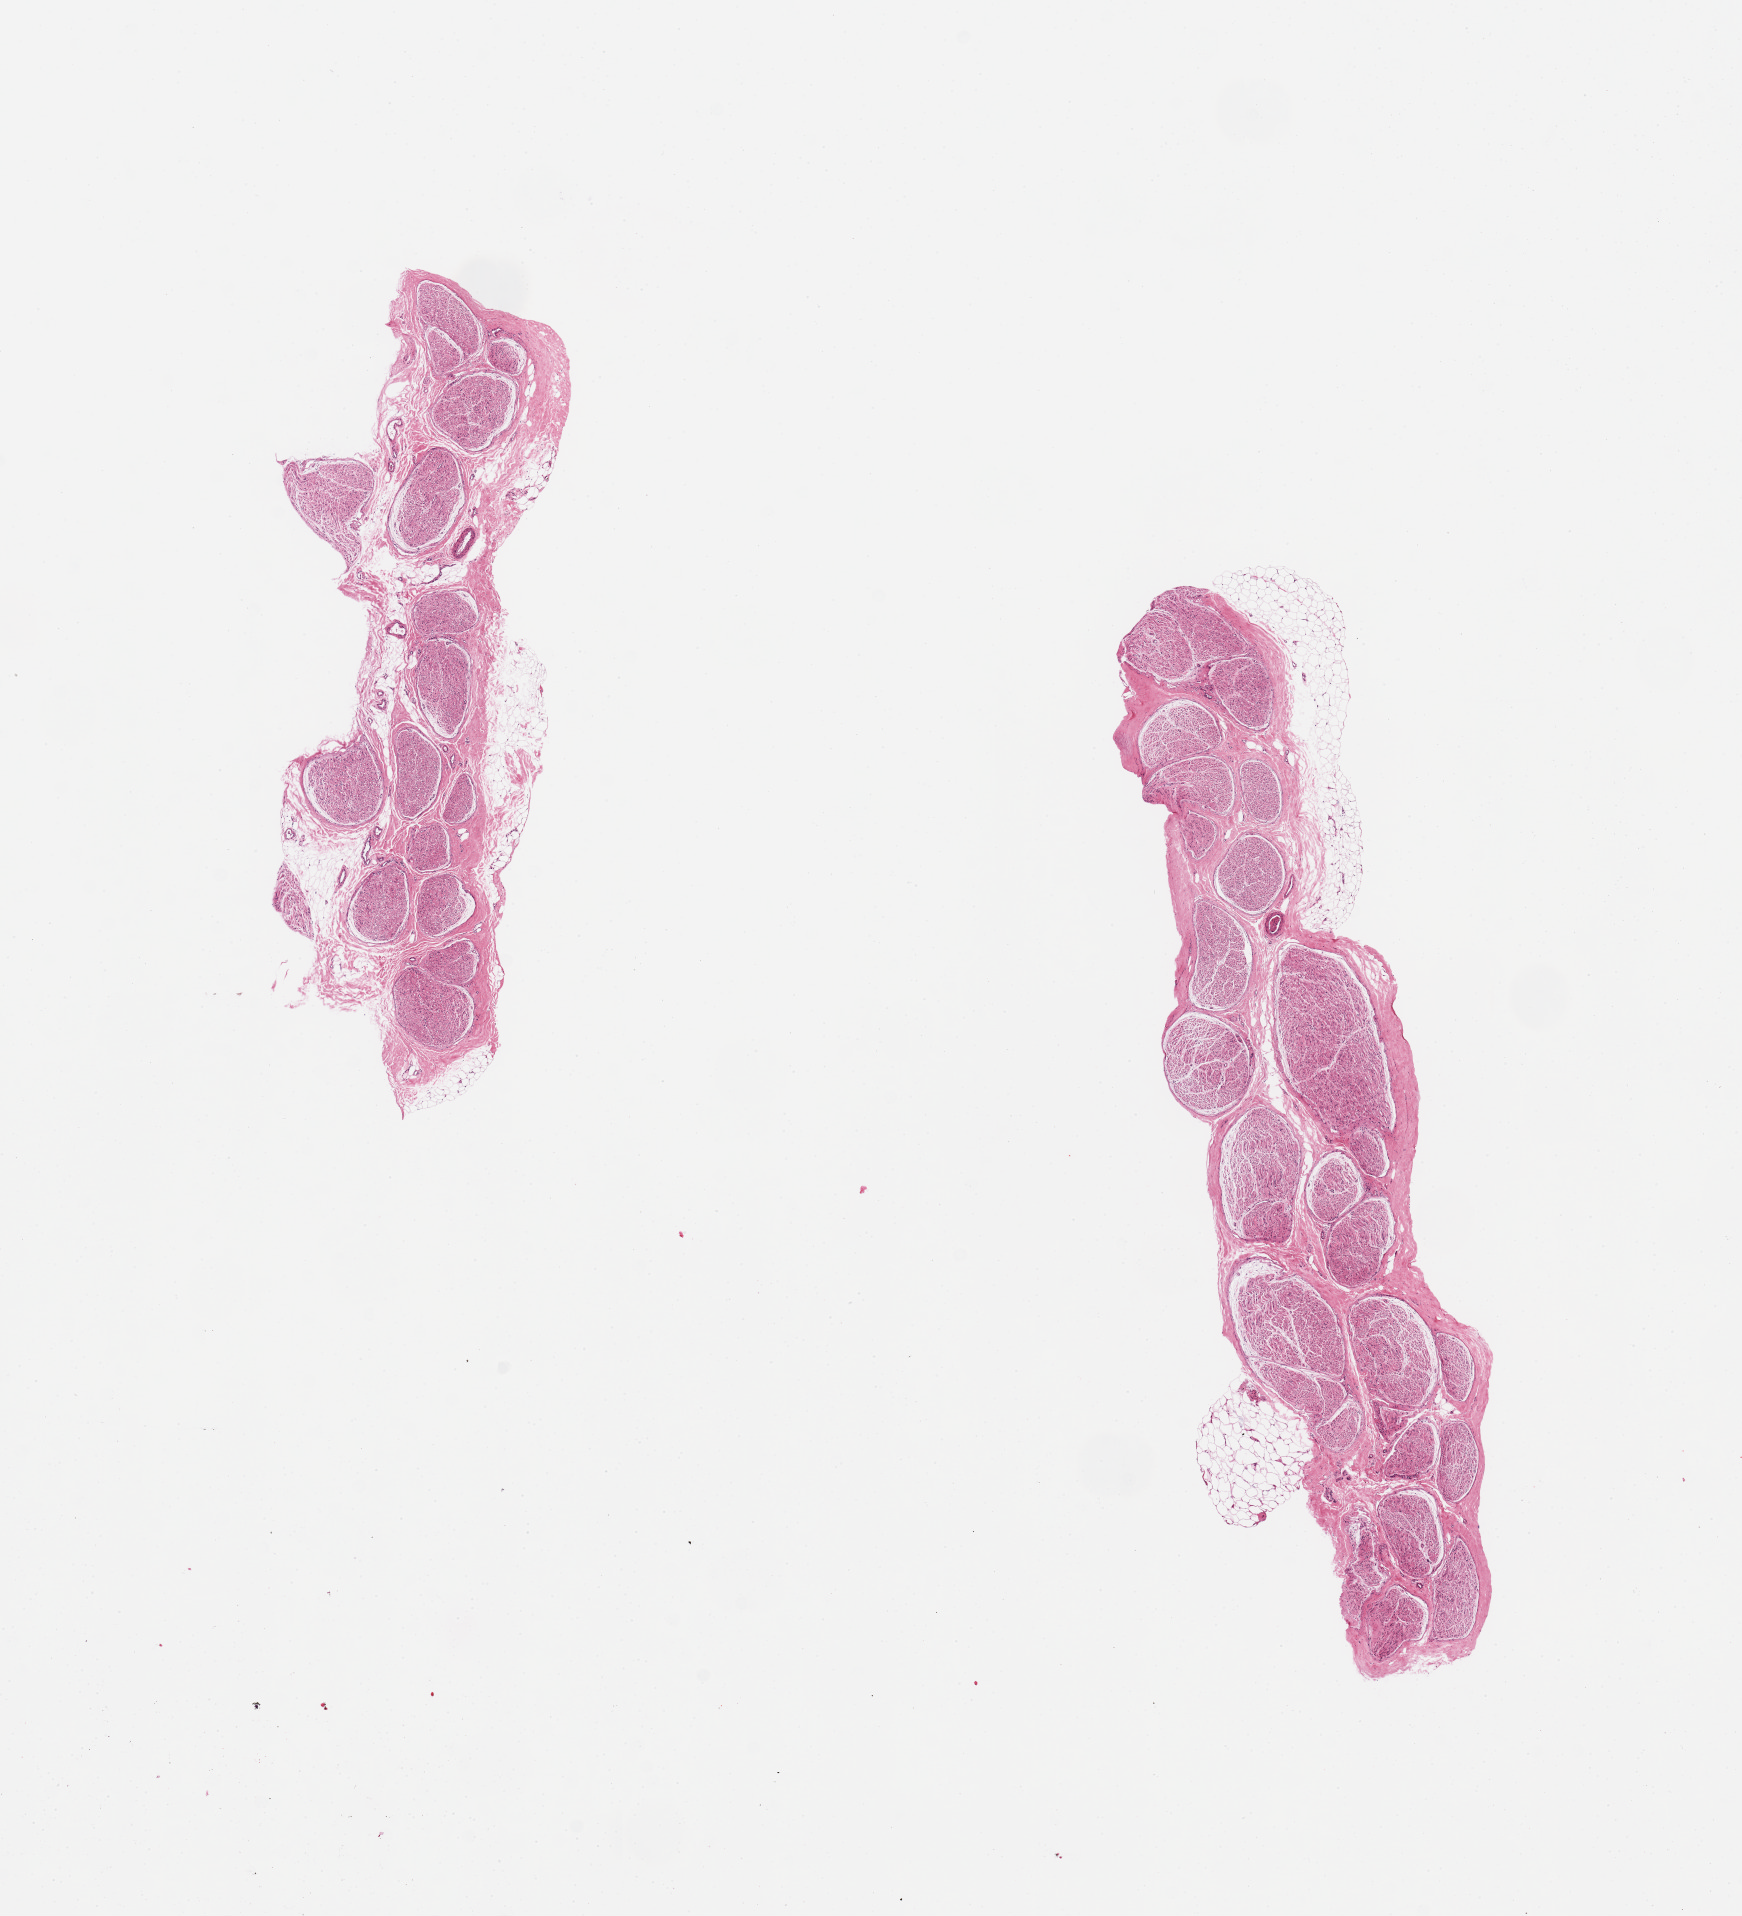
Whole-slide image, haematoxylin and eosin stain, low-resolution overview of the scanned area, about 13.8 x 15.2 mm (acquisition: 20x scan); PAXgene-fixed, paraffin-embedded tissue; target tissue: tibial nerve; donor tissue sample. Female donor.
Review note (as recorded): 2 pieces; small amount of peripheral fat.